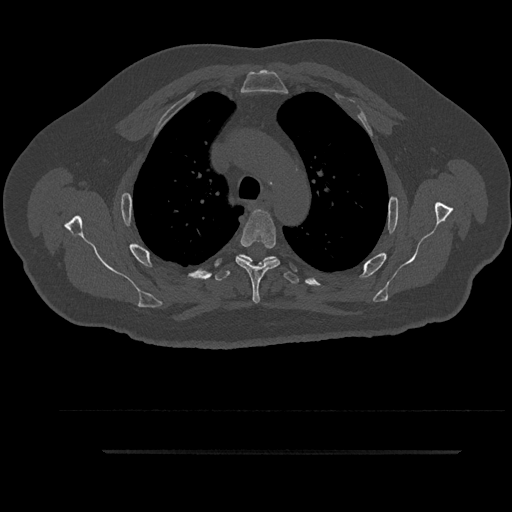
CT including the spine, one axial slice; reconstruction kernel Br40s/3; 120 kVp; bone window (W 1800 / L 400 HU); 0.5 mm slice thickness; 512 × 512 image matrix, field of view 432 × 432 mm. Male patient, age 63 years. From the clinical record (not read from this slice): primary cancer: renal.
Outlined on this slice (semi-automatically segmented with operator editing):
- T4 vertebra: bounding box (x1, y1, x2, y2) in pixels: (235, 210, 280, 304)
- T5 vertebra: (215, 254, 299, 284)